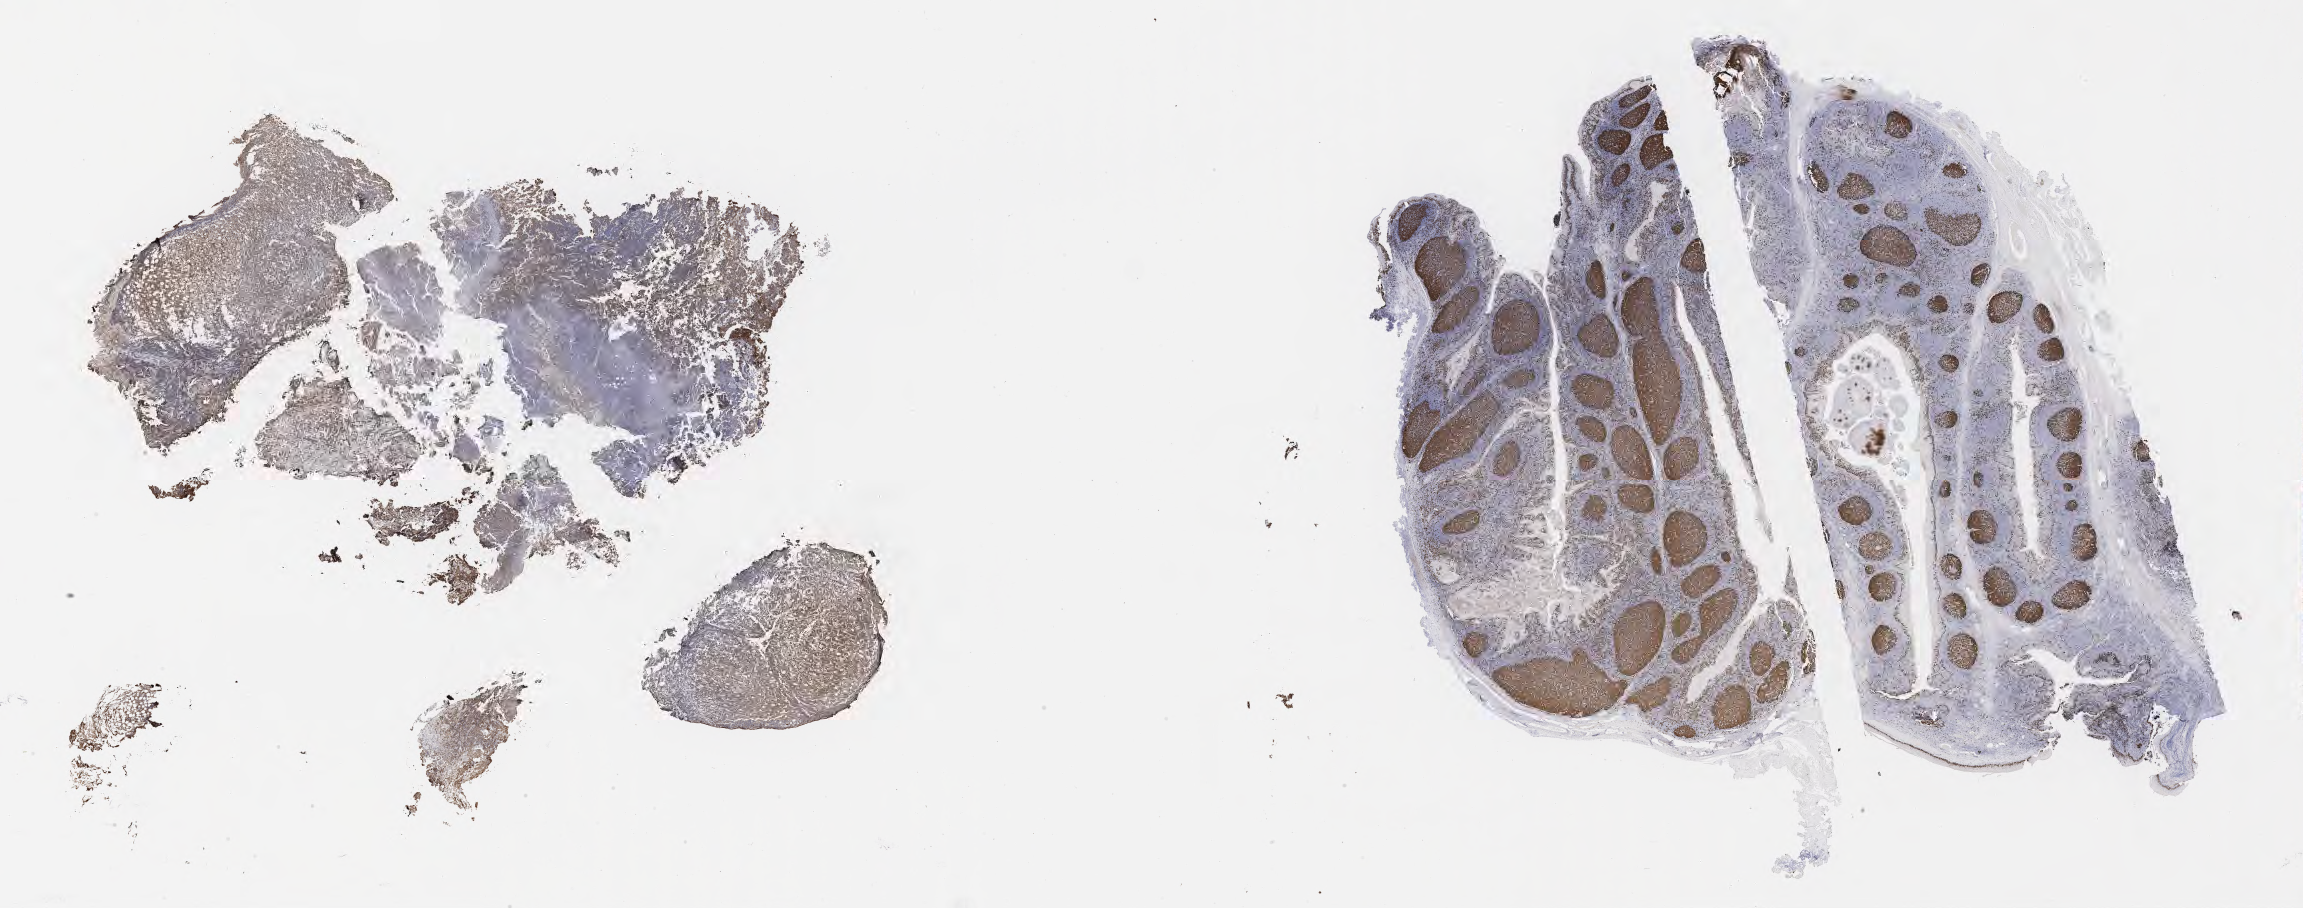
Whole-slide image, immunohistochemical stain for Ki-67 — shown as a low-resolution overview of the whole scanned area (about 37.2 x 14.7 mm); specimen: tumor tissue. Male patient, aged 23.
Histologic diagnosis: Burkitt lymphoma, NOS.